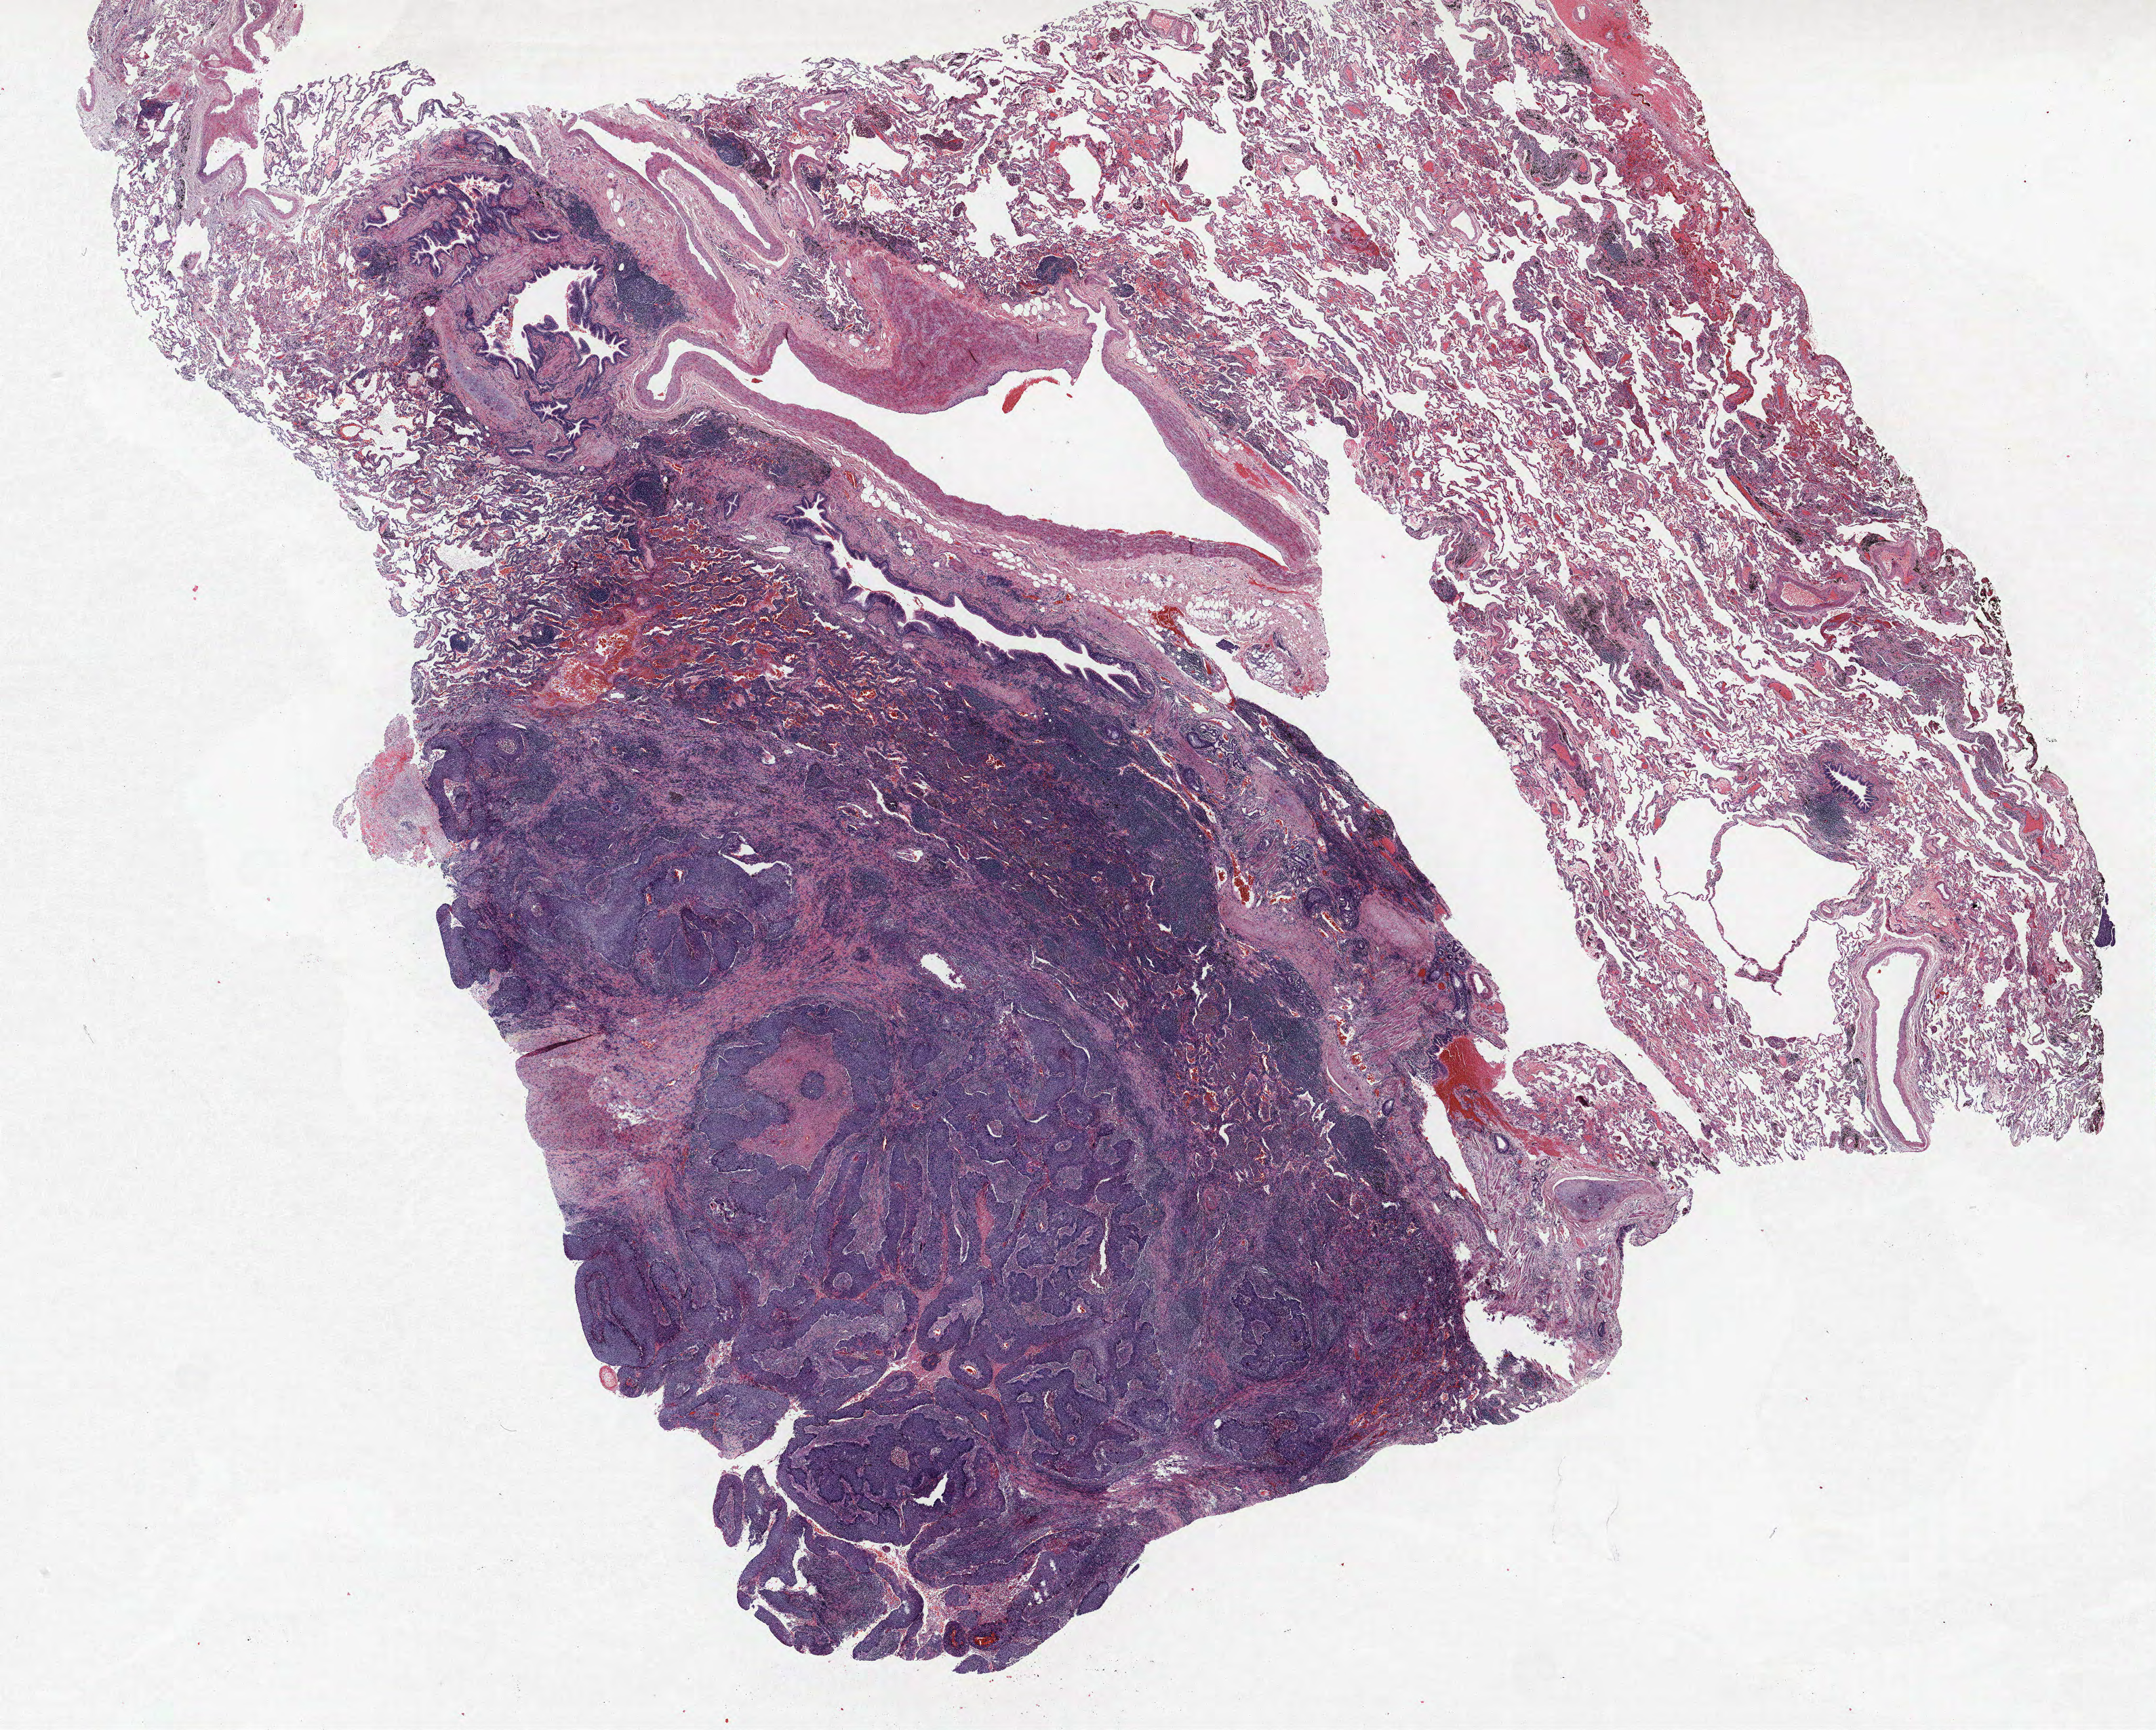
H&E-stained whole-slide image — shown as a low-resolution overview of the whole scanned area (about 25.4 x 20.4 mm); formalin-fixed paraffin-embedded (FFPE) section; lung. Male patient, aged 67 at enrolment. Former smoker at enrolment.
Participant's lung-cancer diagnosis: Squamous cell carcinoma, NOS. Note: participant had 2 primary lung cancers recorded; fields above describe the first.